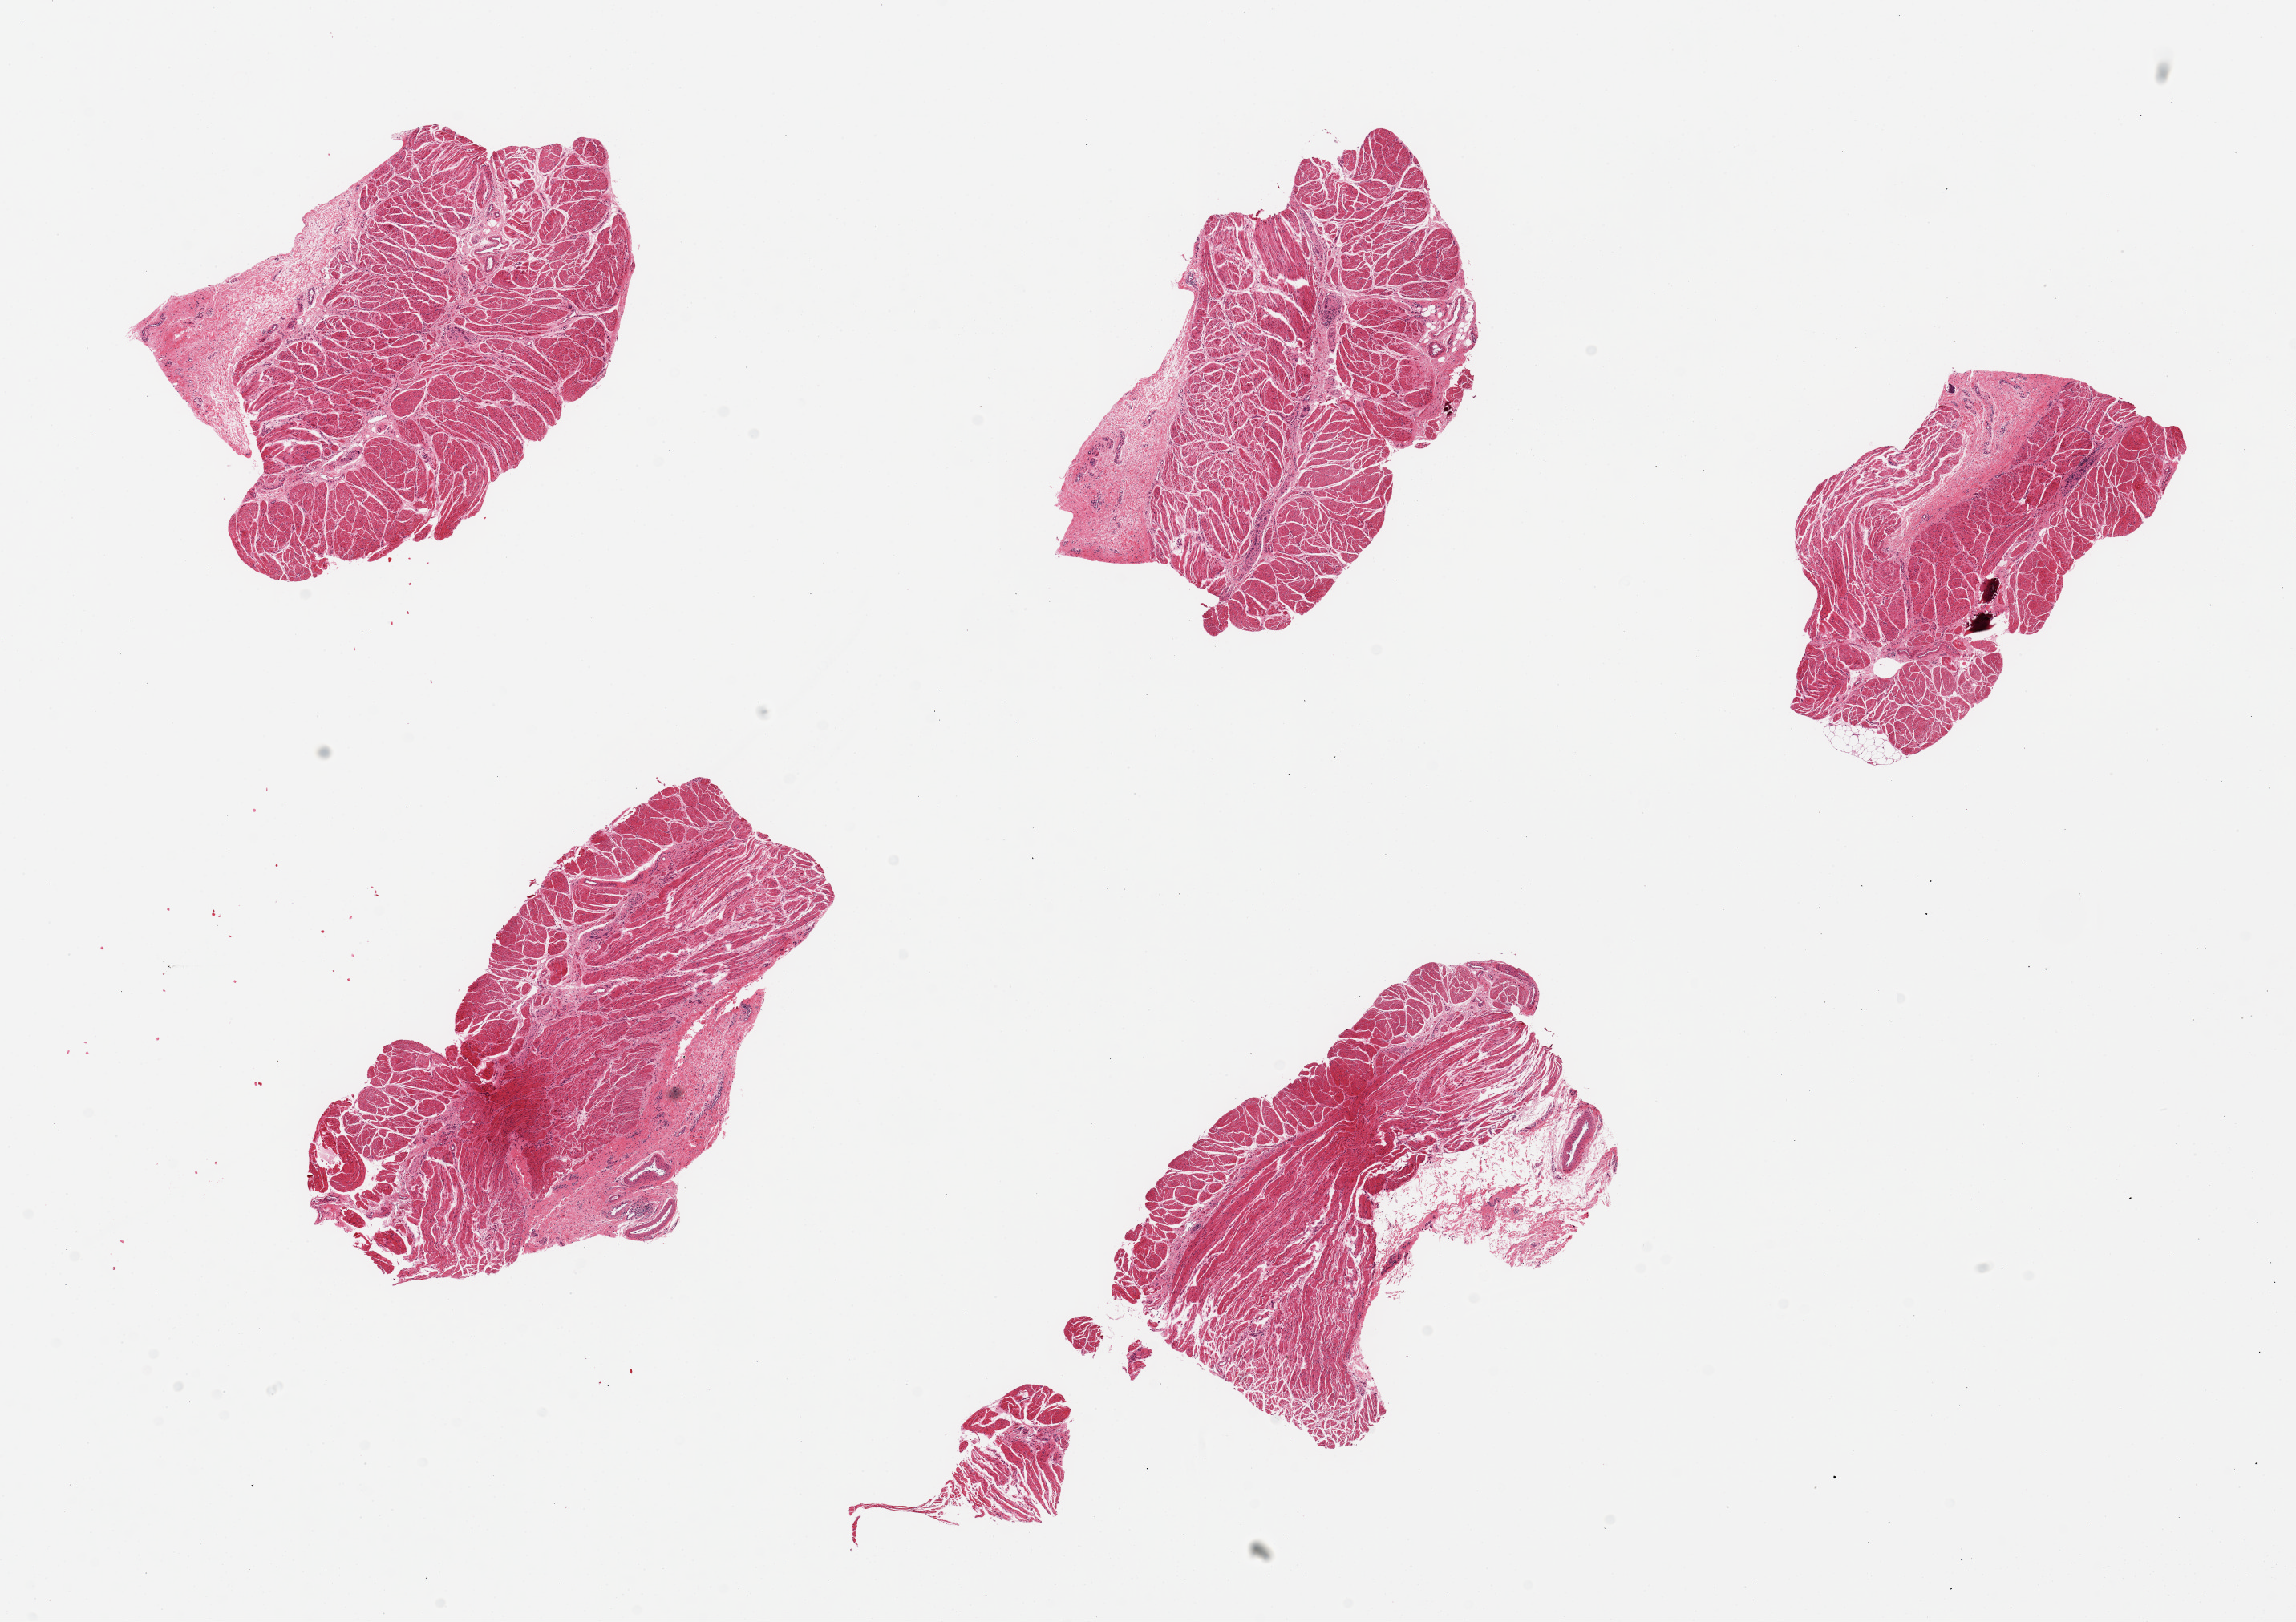
Whole-slide image, haematoxylin and eosin stain, brightfield, whole scanned area (about 22.6 x 16.0 mm, slide scanned at 20x) shown as a low-resolution overview. PAXgene-fixed paraffin-embedded (PFPE) section. Sampled site (target tissue): gastroesophageal junction. Donor tissue sample. Donor: male.
• reviewer comment on this tissue sample: 5 pieces; well dissected except for some focal fat and fibrous tissue